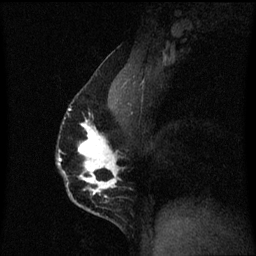
Breast MRI (dynamic contrast-enhanced), one sagittal slice. Position 37 of 60 along the scan axis. Dynamic contrast-enhanced series, image 2 of 3 at this slice position (ordered by acquisition). 1.5 T. TE 4.2 ms, TR 8.4 ms. 2 mm slice thickness. 256 × 256 image matrix, field of view 200 × 200 mm. Patient: female, 40 years.
Outlined on this slice (semi-automatic segmentation, software-assisted and operator-edited):
- analysis volume of interest (the breast-tissue region the enhancement analysis was run in; not a lesion): bounding box (x1, y1, x2, y2) in pixels: (57, 84, 125, 211)
- tumour enhancement mask (voxels above the 70 % enhancement threshold inside the analysis volume of interest): (57, 110, 121, 203)